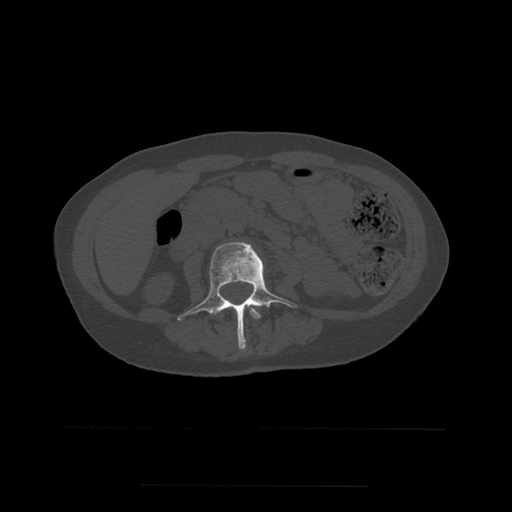
CT including the spine, one axial slice. Slice 192 of 544 in the series (ordered by position). Bone window (W 1800 / L 400 HU). 512 × 512 image matrix, field of view 350 × 350 mm. Patient age 58 years. From the clinical record (not read from this slice): primary cancer: lung.
Annotated regions visible in this slice (semi-automatically segmented with operator editing):
- L2 vertebra: bounding box (x1, y1, x2, y2) in pixels: (249, 306, 261, 320)
- L3 vertebra: (177, 242, 297, 350)